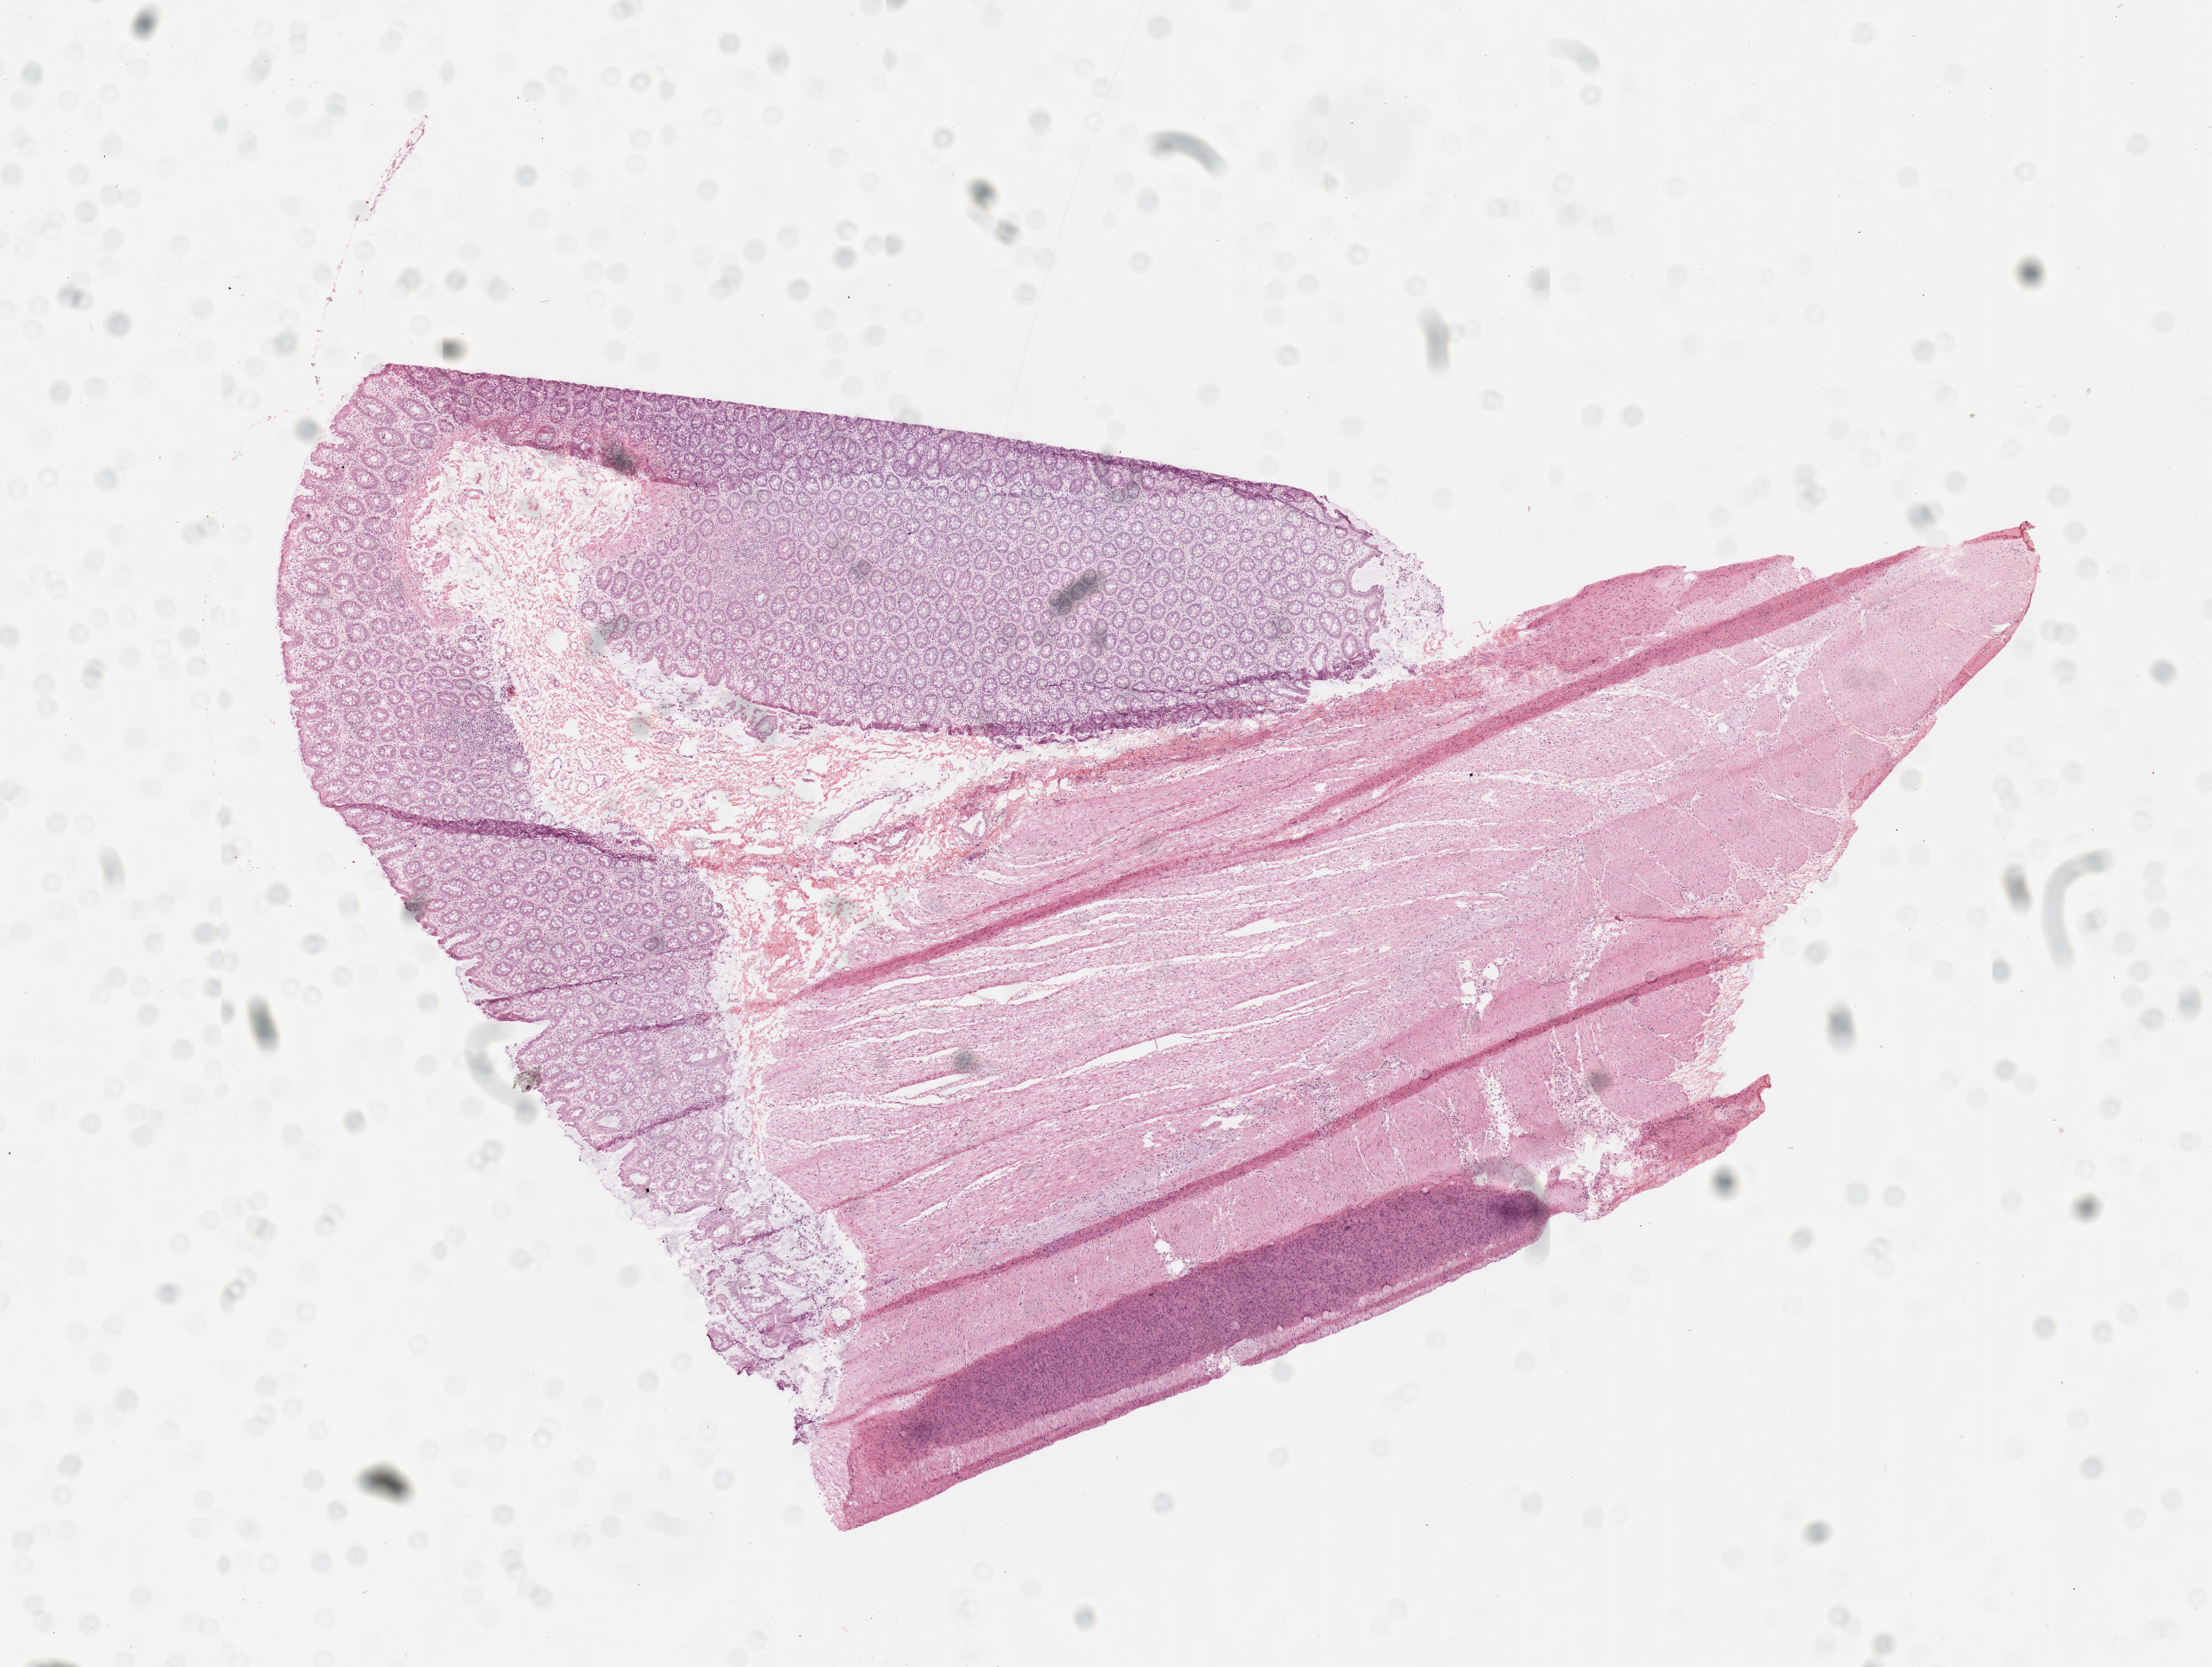
Whole-slide histology image, H&E-stained, low-resolution overview of the scanned area, about 10.0 x 7.6 mm (from a 20x scan), frozen section from the top of the tissue portion, sample: solid tissue normal (non-tumour tissue), colon. Female patient; age at initial diagnosis 77 years.
• this section: solid tissue normal sample (biorepository sample class)
• patient diagnosis: Adenocarcinoma, NOS (sigmoid colon)